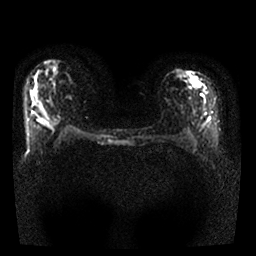
Breast MRI, one axial slice; position 11 of 25 along the scan axis; diffusion-weighted series; image 2 of 4 stored at this slice position (different b-values; order by instance number); 1.5 T; 256 × 256 image matrix. Female patient.
Annotated regions visible in this slice (manually delineated by an expert):
- tumour on diffusion-weighted imaging: bounding box (x1, y1, x2, y2) in pixels: (194, 77, 202, 87)